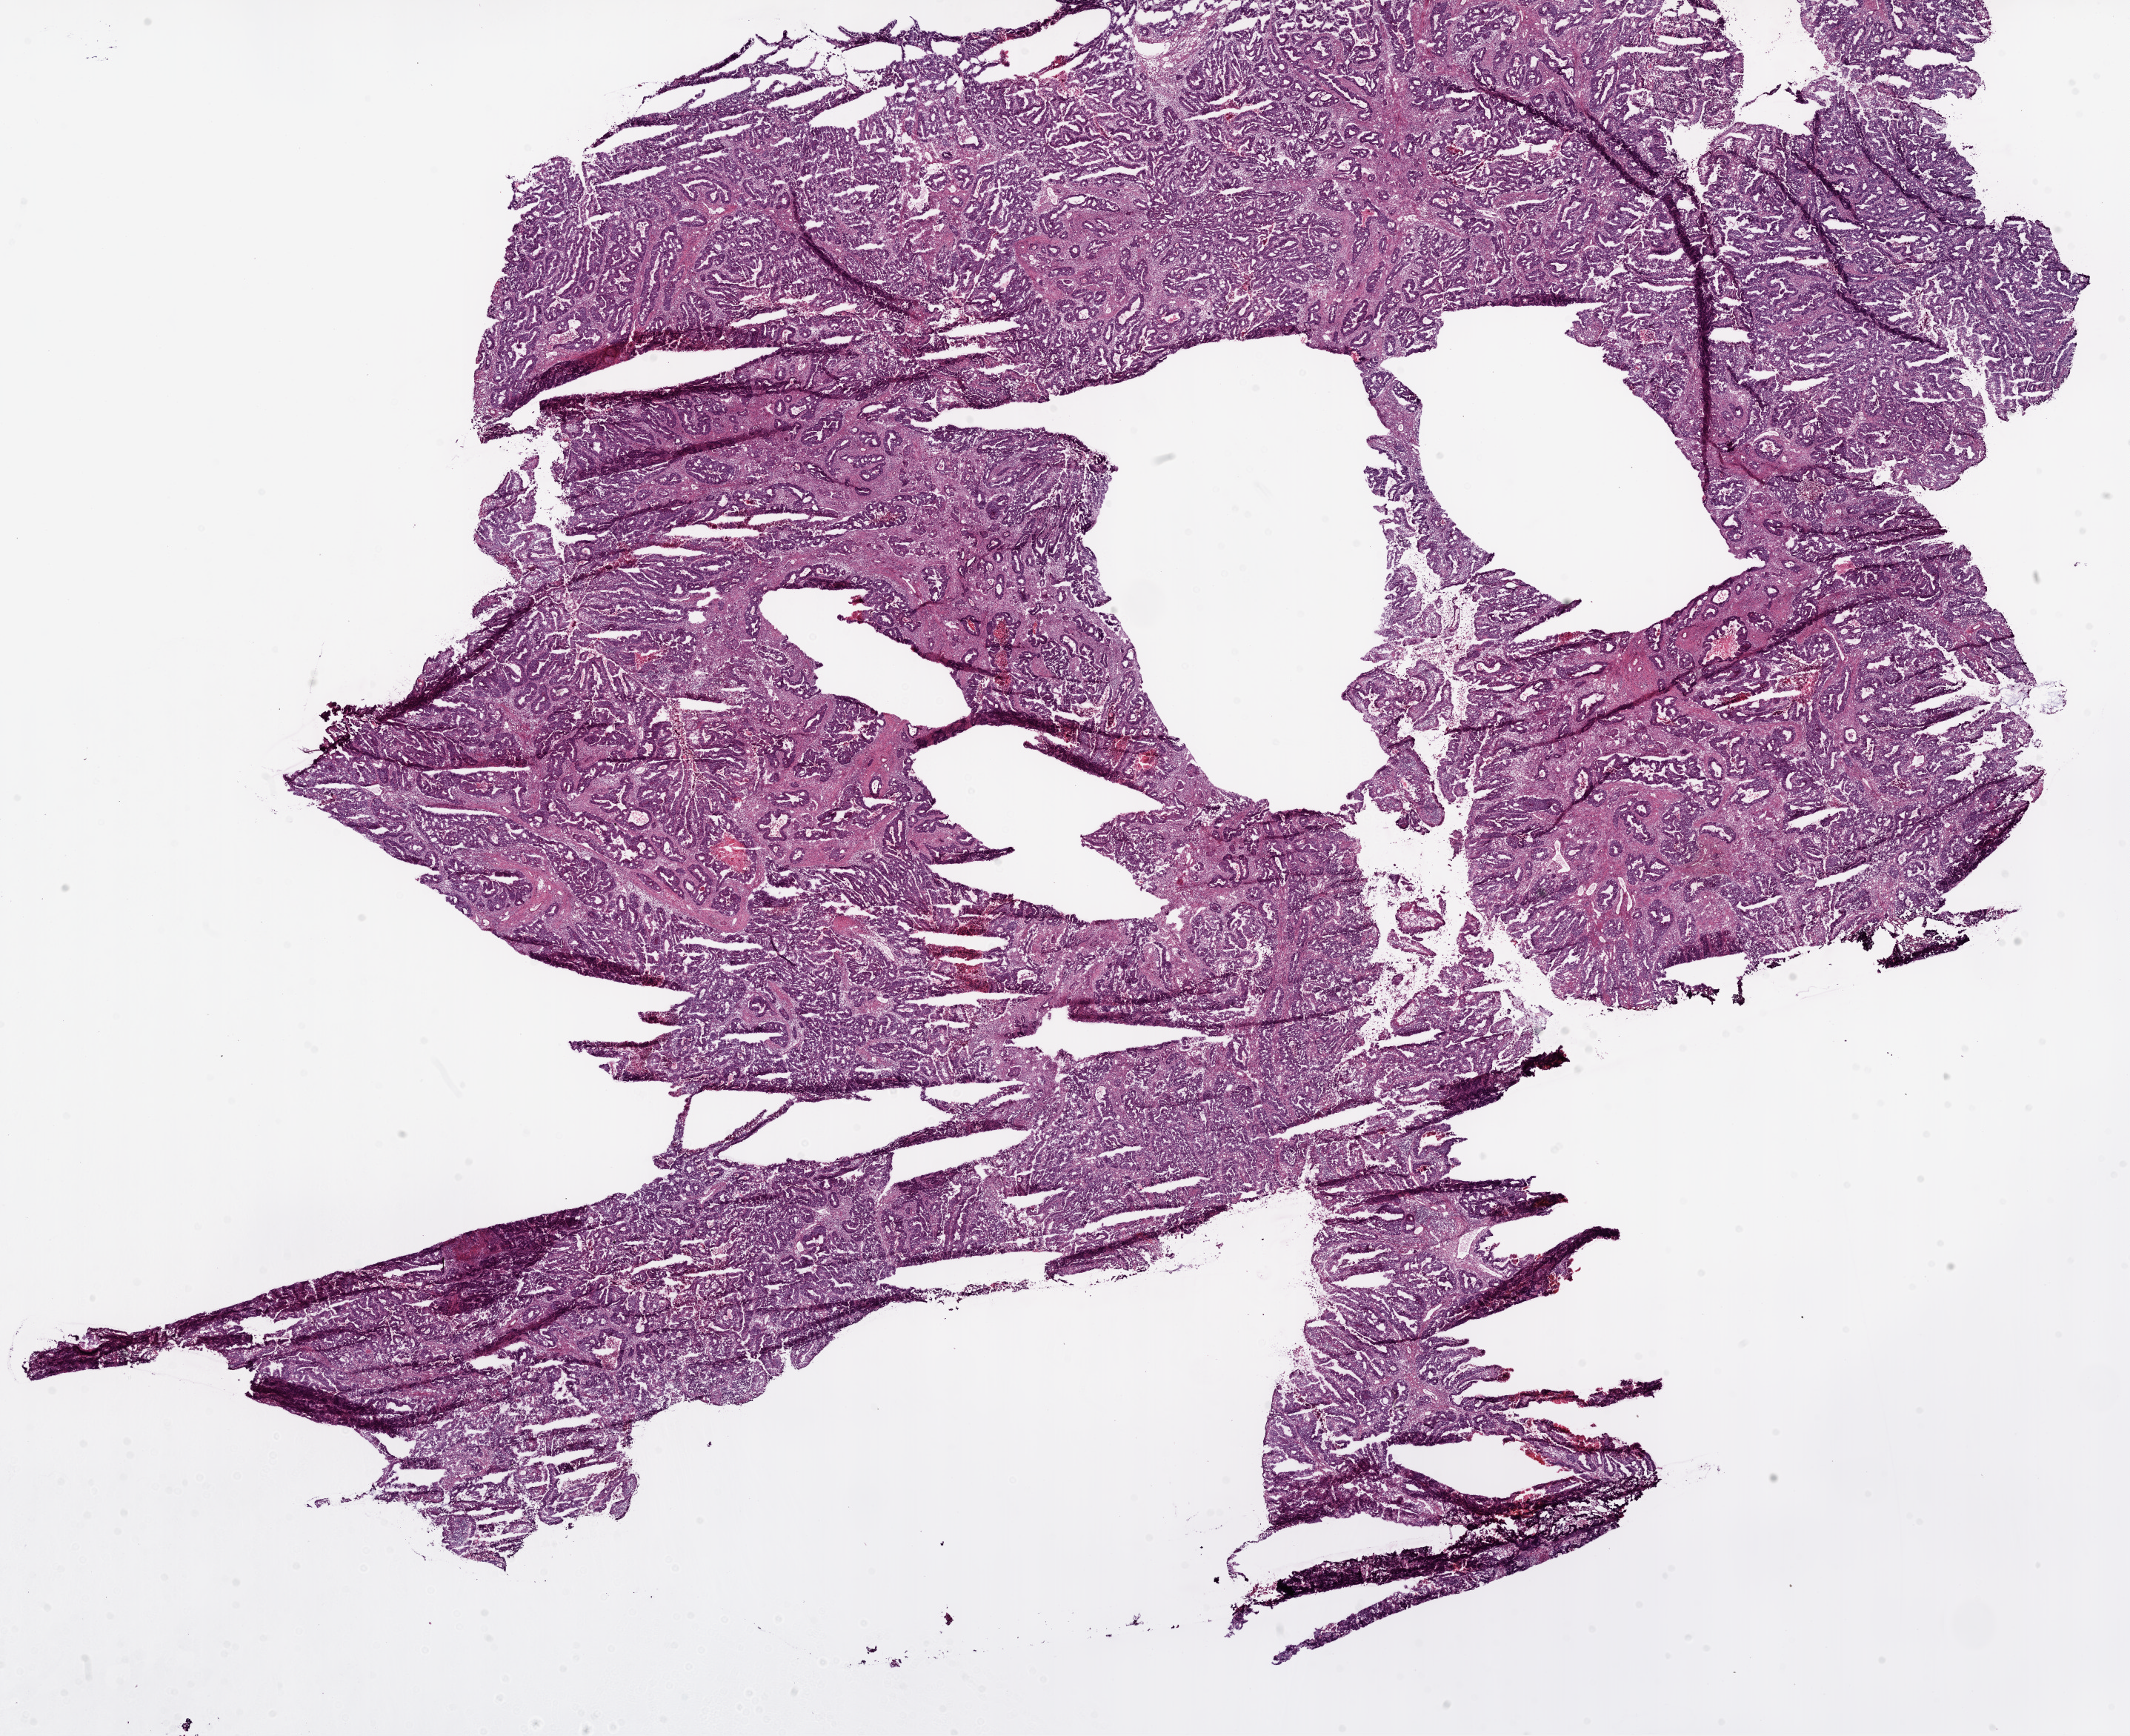
Hematoxylin and eosin (H&E) stained whole-slide image, whole scanned area (about 23.1 x 18.8 mm) shown as a low-resolution overview, frozen section from the bottom of the tissue portion, rectum, primary tumour sample. Male patient; age at initial diagnosis 57 years. Composition of this section per pathologist review: tumour cells 80%, tumour nuclei 75%, normal cells 0%, stromal cells 15%, necrosis 5%.
AJCC pathologic stage: I (7th edition). Pathologic diagnosis: Adenocarcinoma, NOS (rectosigmoid junction). TNM: T2 N0 M0. Lymph nodes positive (case pathology): 0 of 16 examined.